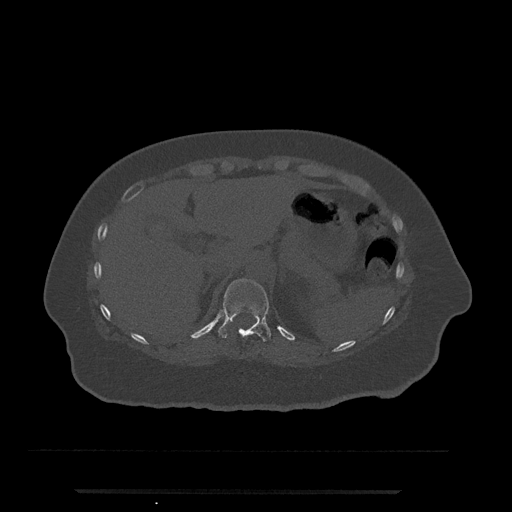
CT including the spine, one axial slice. Position 231 of 797 along the scan axis. Reconstruction kernel Br40s/3. 120 kVp. Bone window (W 1800 / L 400 HU). 0.5 mm slice thickness. 512 × 512 image matrix, field of view 440 × 440 mm. Patient: female, 51 years. From the clinical record (not read from this slice): primary cancer: neuro; vertebrae with lytic lesions (as recorded): T8.
Annotated regions visible in this slice (semi-automatically segmented with operator editing):
- T11 vertebra: bounding box <218,278,271,342> (left, top, right, bottom; pixels)